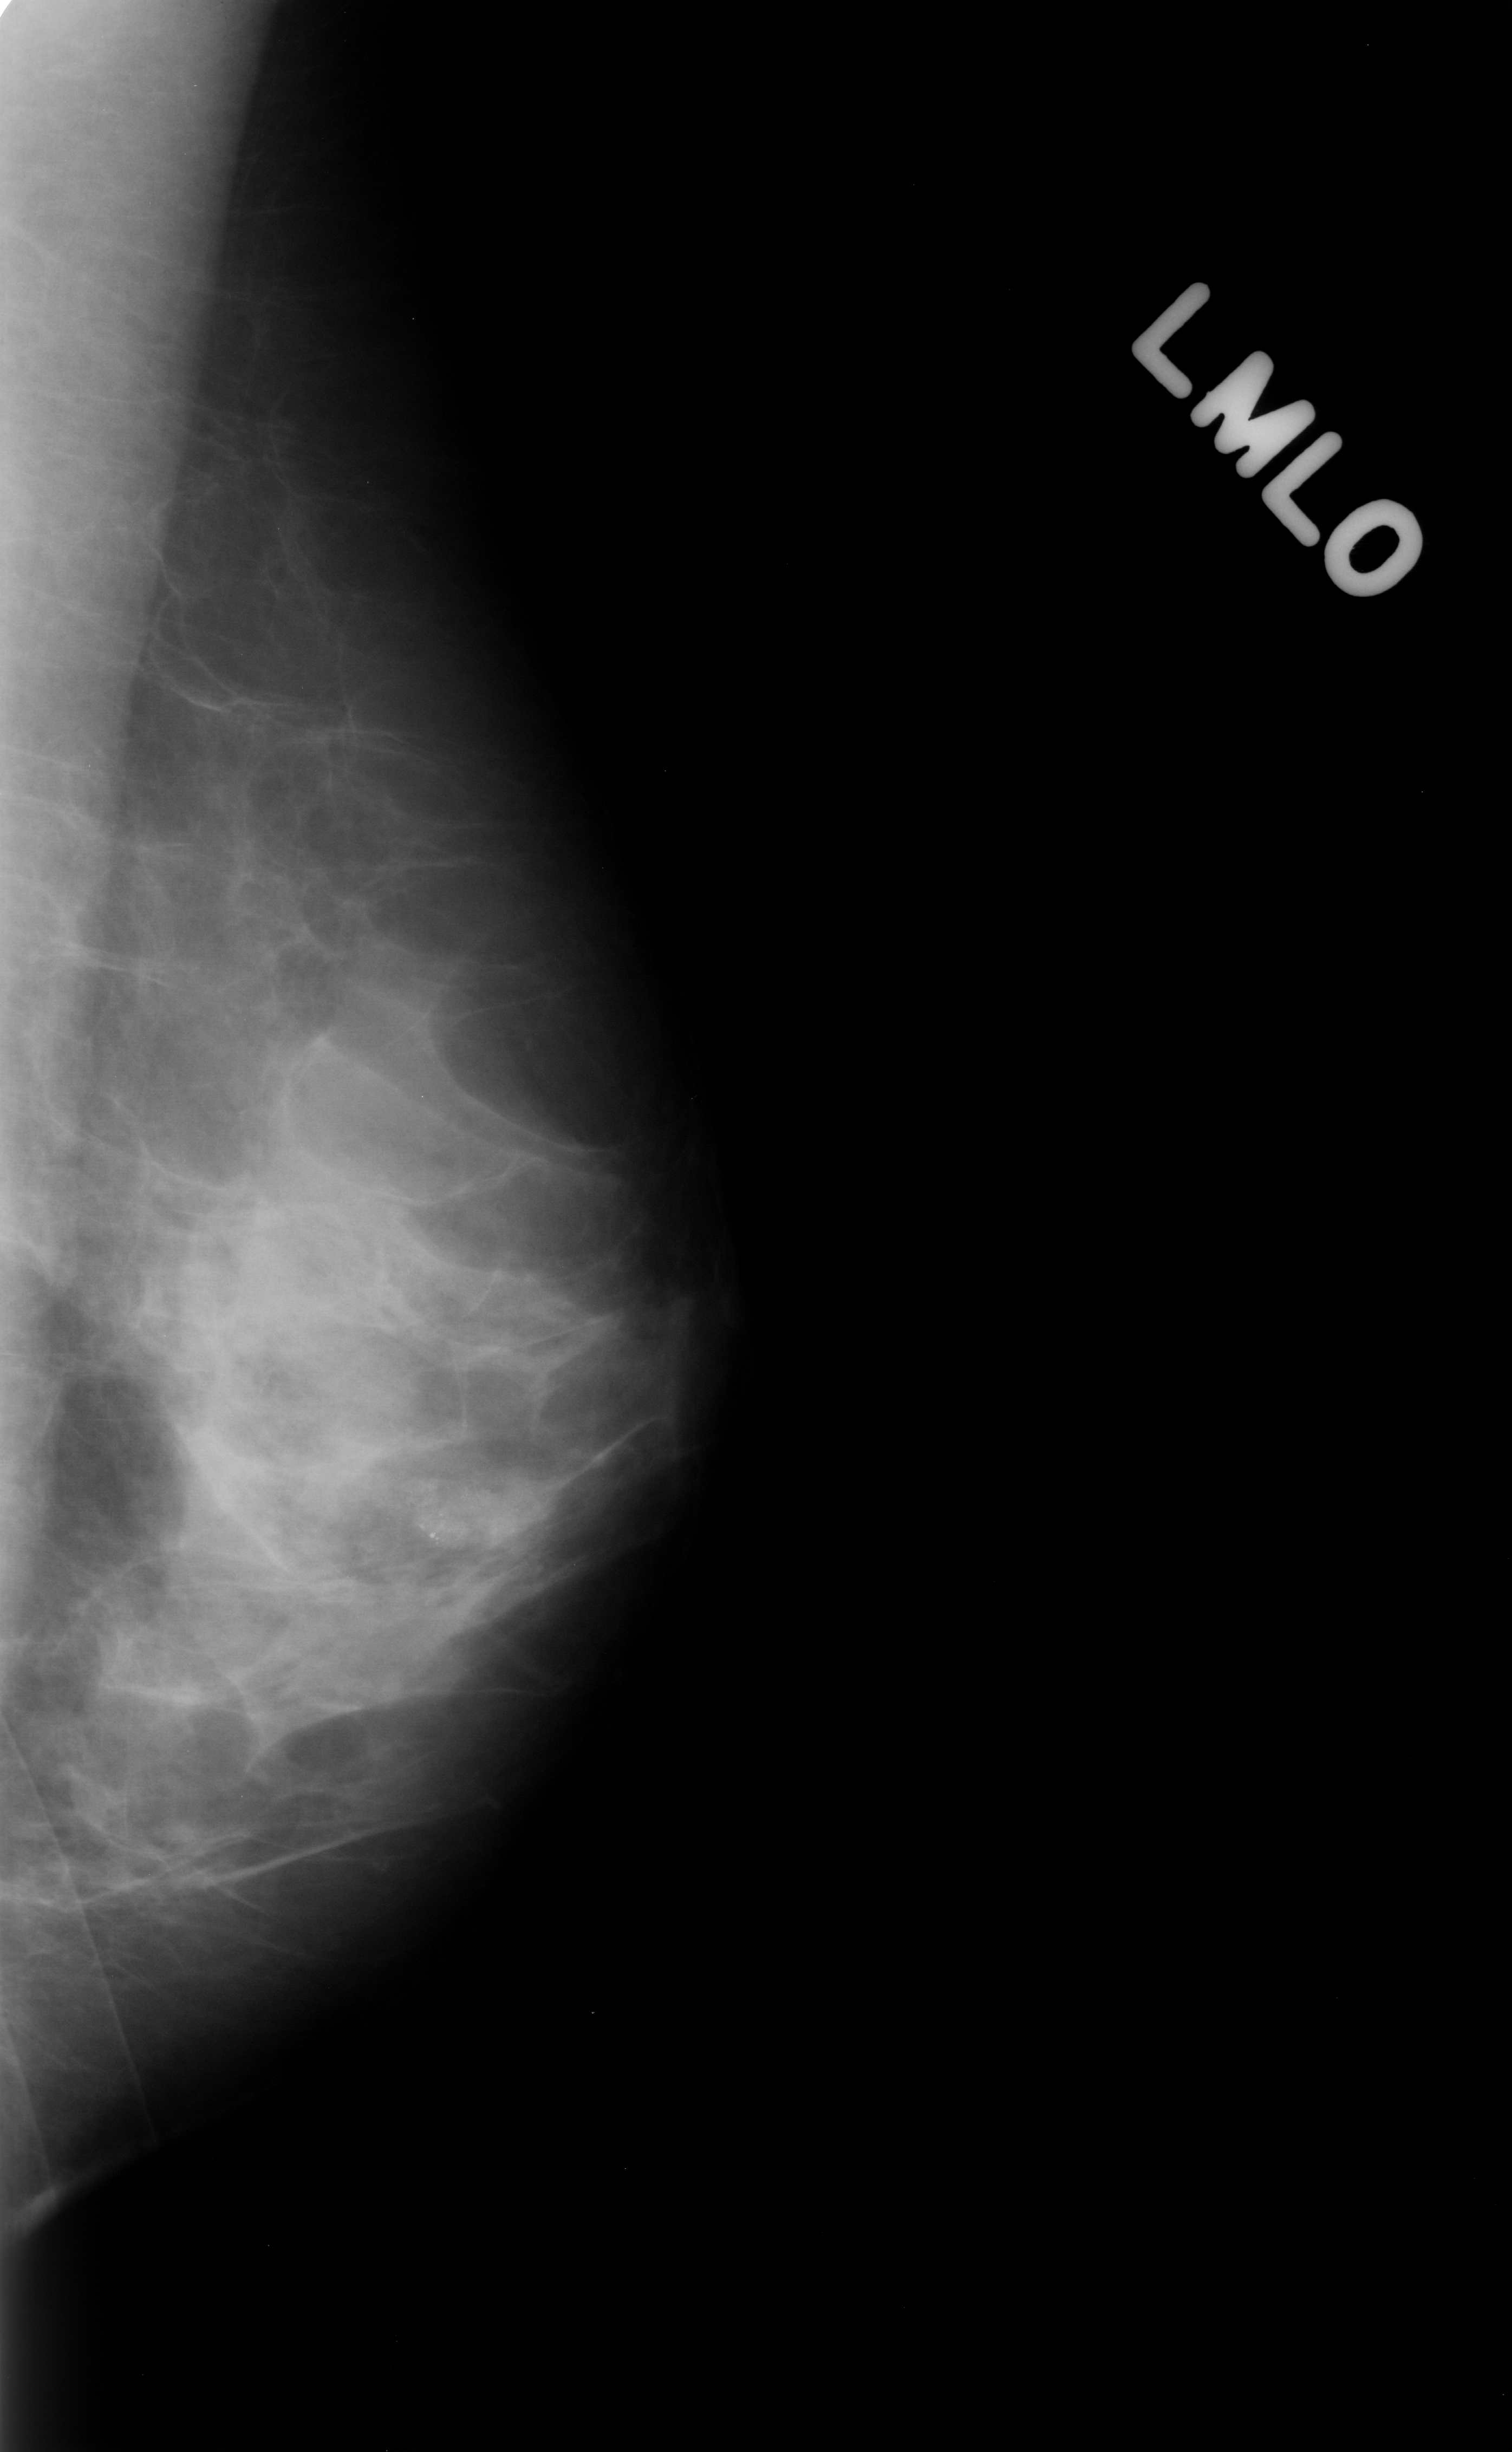
Digitized screen-film mammogram. Left breast. MLO view. BI-RADS breast density category 3 (scale 1–4). 1512 × 2452 image matrix.
Expert-marked regions of interest on this film, with their recorded descriptors:
- calcifications, morphology pleomorphic, distribution clustered; BI-RADS assessment category 4; subtlety rating 3 on a 1 (subtle) to 5 (obvious) scale; pathology result (as recorded, not read from the image): benign: bounding box (x1, y1, x2, y2) in pixels: (381, 1446, 521, 1613)